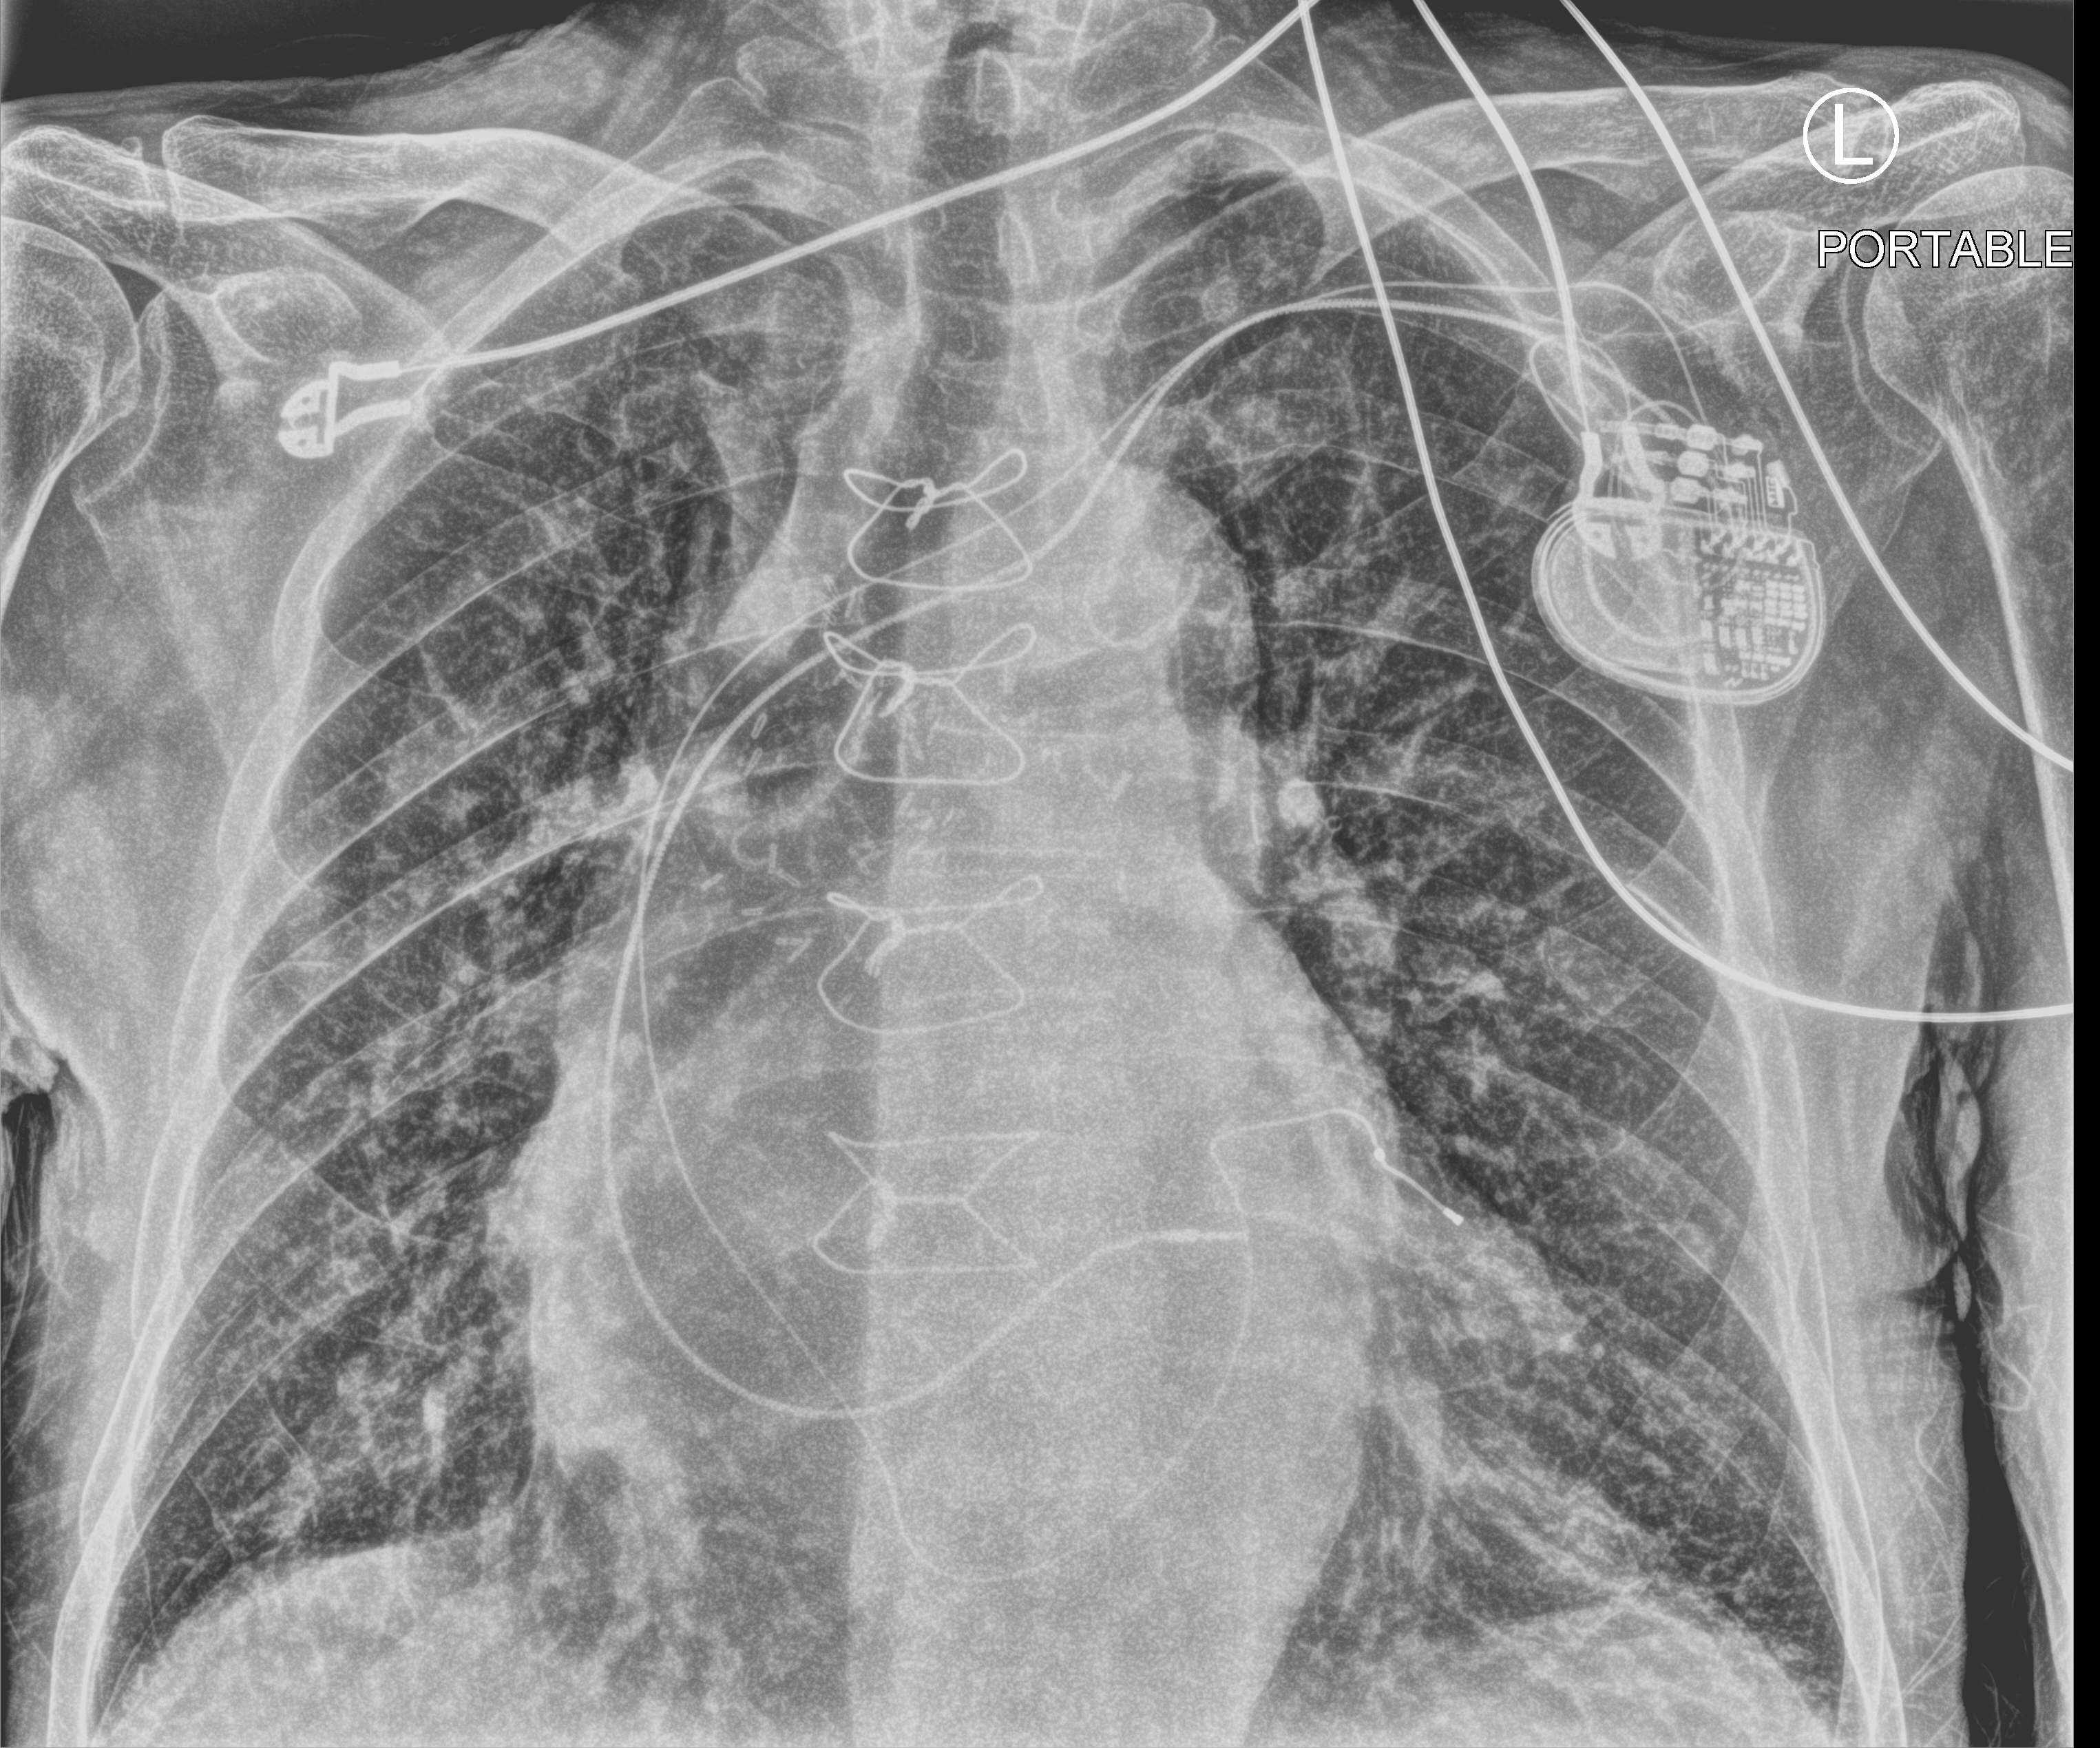
Chest X-ray (portable), anteroposterior (AP) projection. Male patient hospitalised with COVID-19, age 75–90 years.
Hospital-stay facts (about this admission, not read from this image; timing relative to this image not recorded):
- admitted to intensive care during this hospital stay: no
- smoking status (admission record): never
- length of hospital stay: 7 days